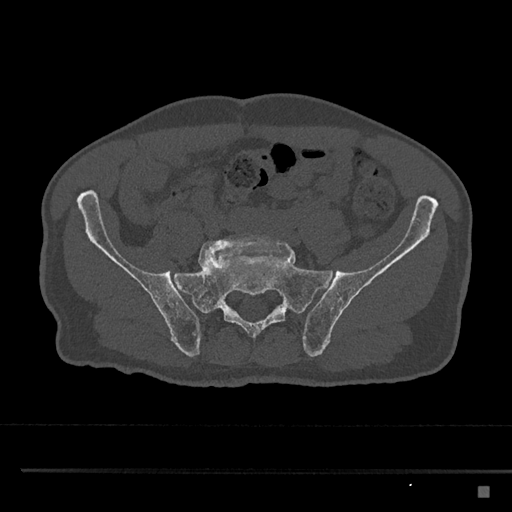
CT including the spine, one axial slice. Reconstruction kernel Br40s/3. 120 kVp. Bone window (W 1800 / L 400 HU). 512 × 512 image matrix, field of view 391 × 391 mm. Patient: male, 59 years. Case-level facts recorded for this patient, not image findings: primary cancer: prostate.
Annotated regions visible in this slice (semi-automatic segmentation, software-assisted and operator-edited):
- L5 vertebra: bounding box [x1, y1, x2, y2] px = [198, 234, 289, 268]